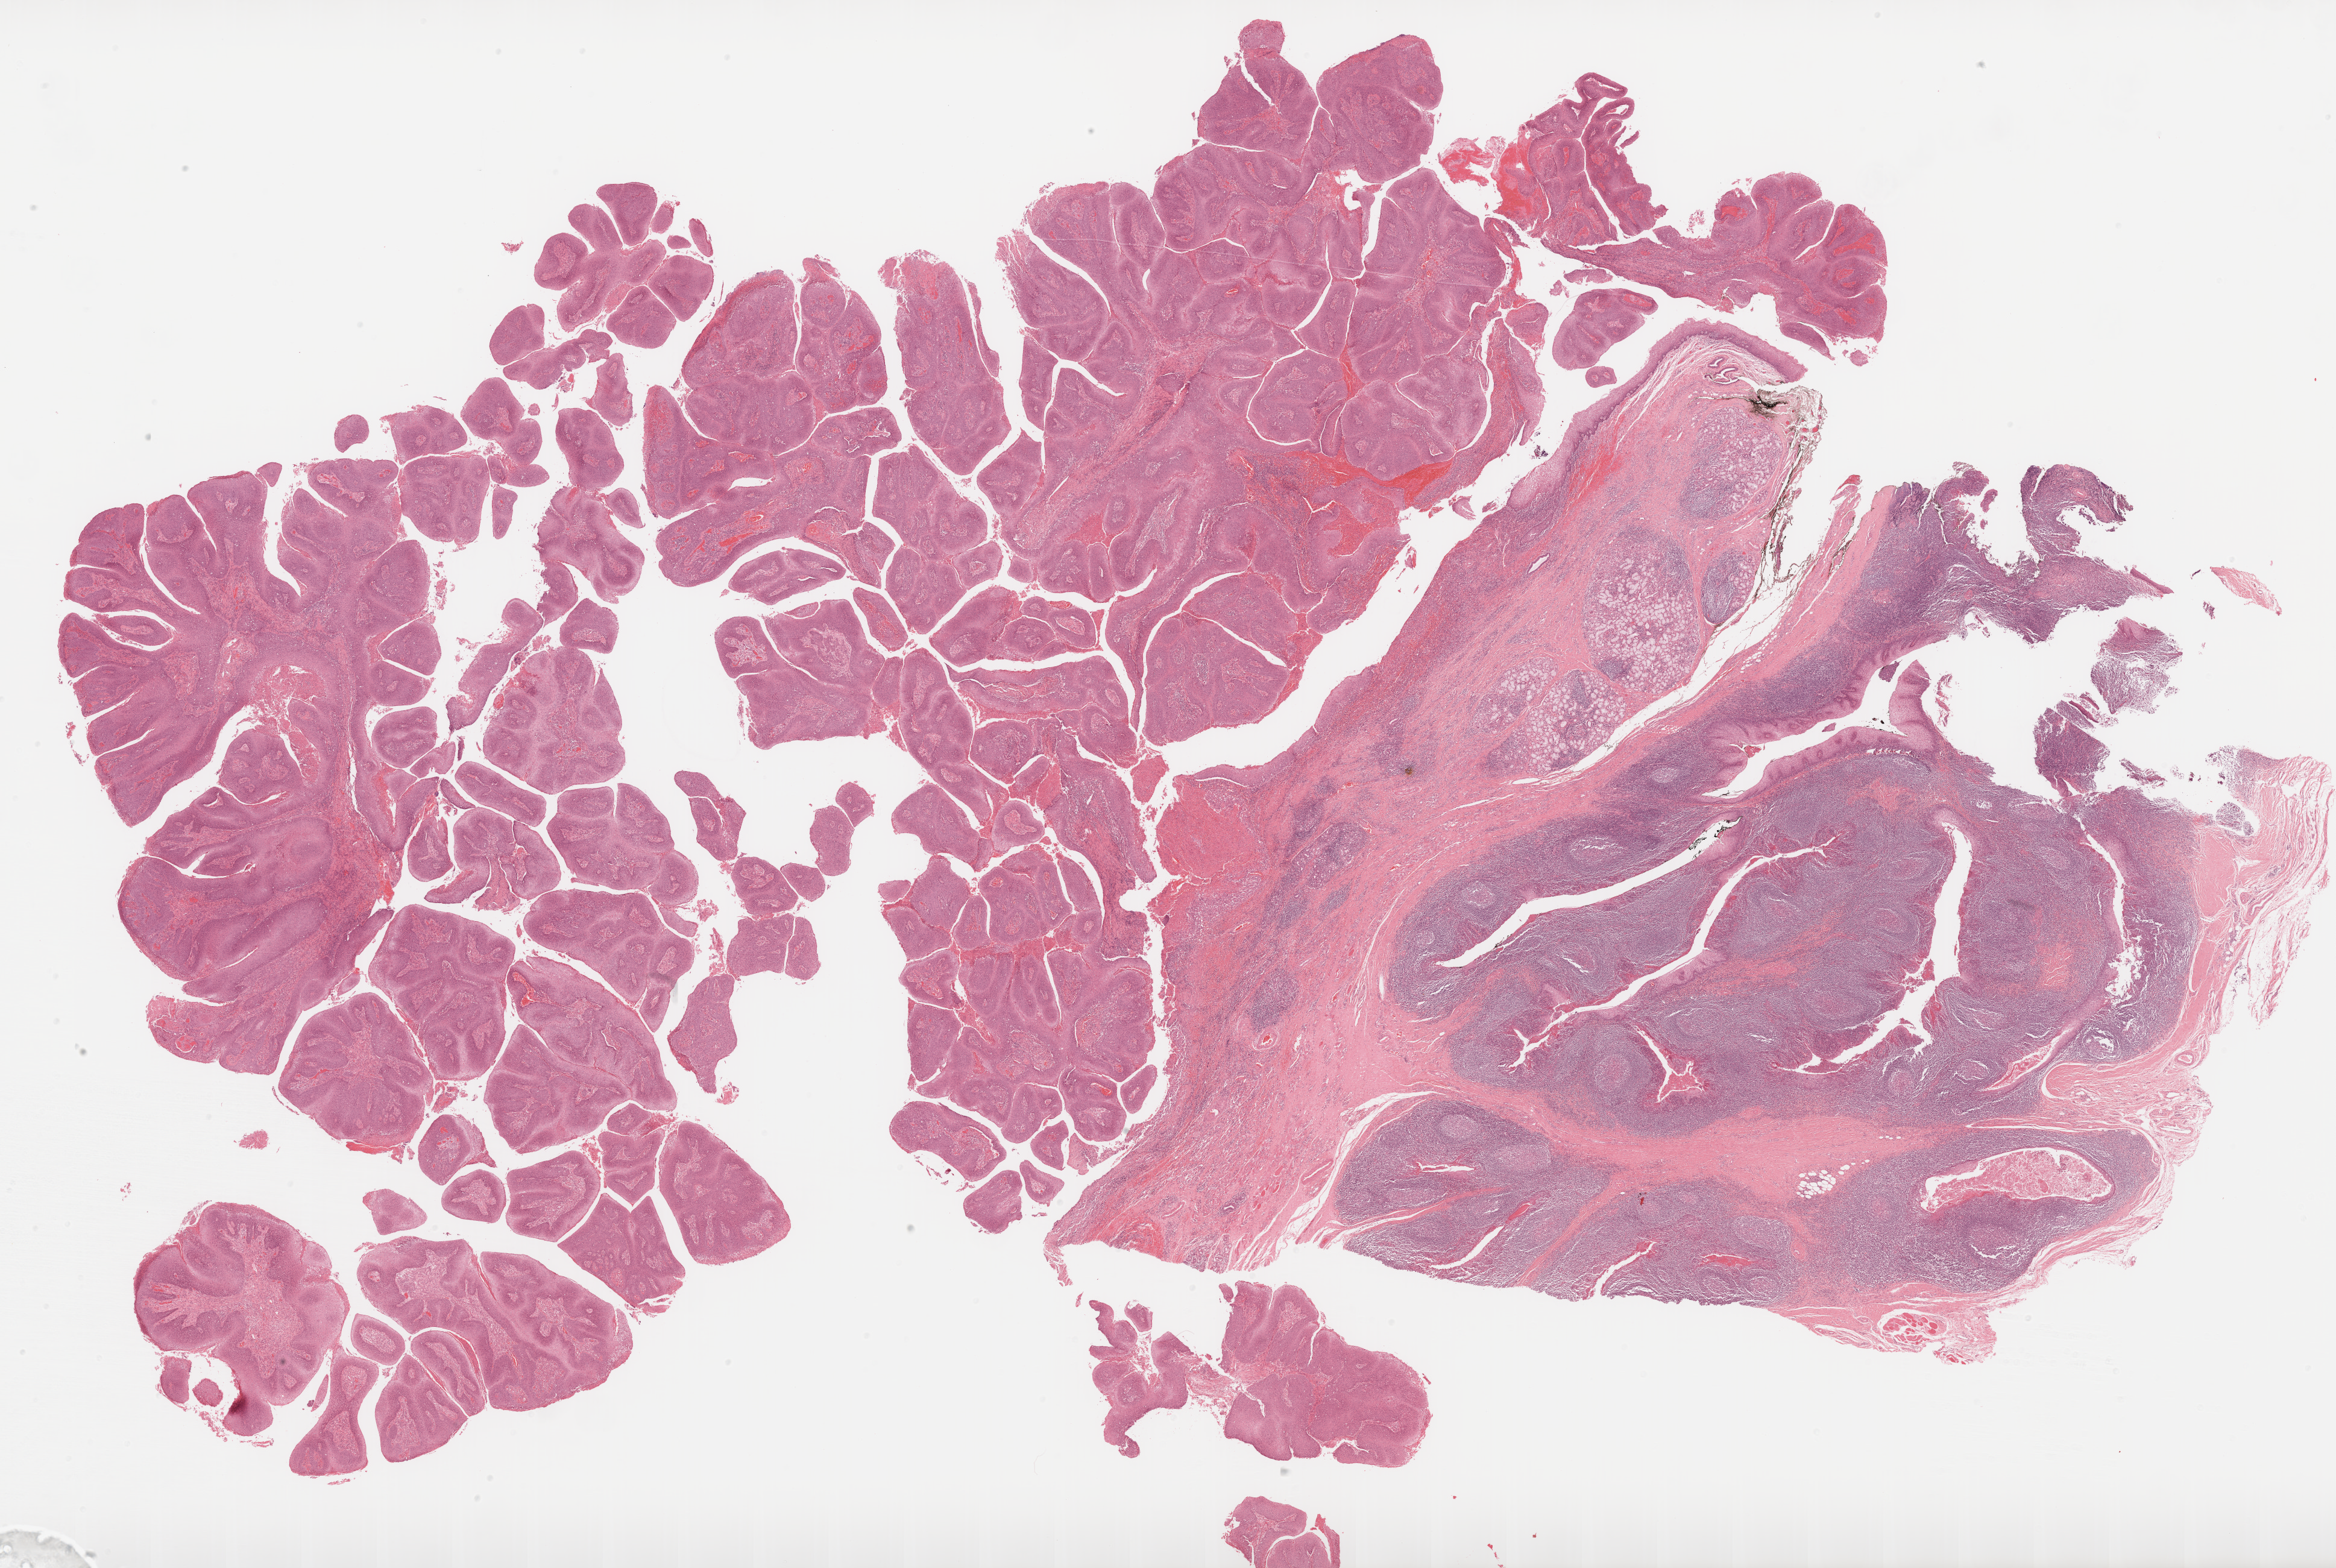
Whole-slide histology image, H&E, shown as a low-resolution overview of the whole scanned area (about 31.1 x 20.9 mm), FFPE section, head and neck, primary tumour sample. Patient: male, age at initial diagnosis 59 years. Histologic grade: G2 (moderately differentiated).
• lymph nodes positive (case pathology): 0 of 24 examined
• diagnosis: Squamous cell carcinoma, NOS (overlapping lesion of lip, oral cavity and pharynx)
• laterality: left
• AJCC pathologic stage: III (6th edition)